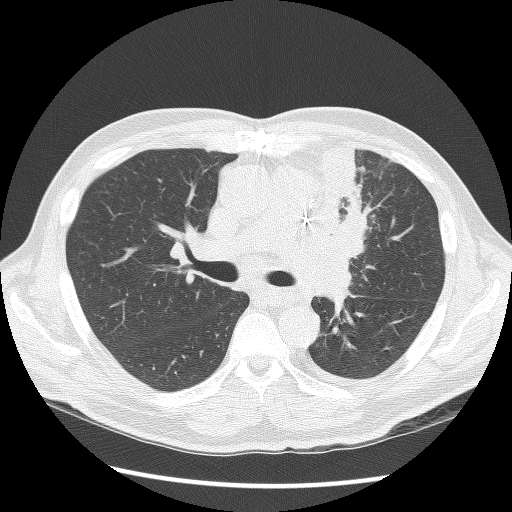
Axial slice from a low-dose chest CT screening exam; second screening round (one year after baseline); lung window (W 1500 / L -600 HU); 2.5 mm slice thickness; lung (sharp) reconstruction kernel (BONE); slice 50 of 136 in the series. Male participant, aged 64 years at enrolment. Former smoker at enrolment.
Expert-annotated lung lesion, box from (x=302, y=147) to (x=383, y=283) px. Screening reader's record for this exam: no non-calcified nodule ≥4 mm recorded. Official screen result: positive, other. Participant outcome: lung cancer diagnosed 24 days after this screen — small cell carcinoma, NOS, left upper lobe, stage IV (AJCC 6th edition), 100 mm at pathology.